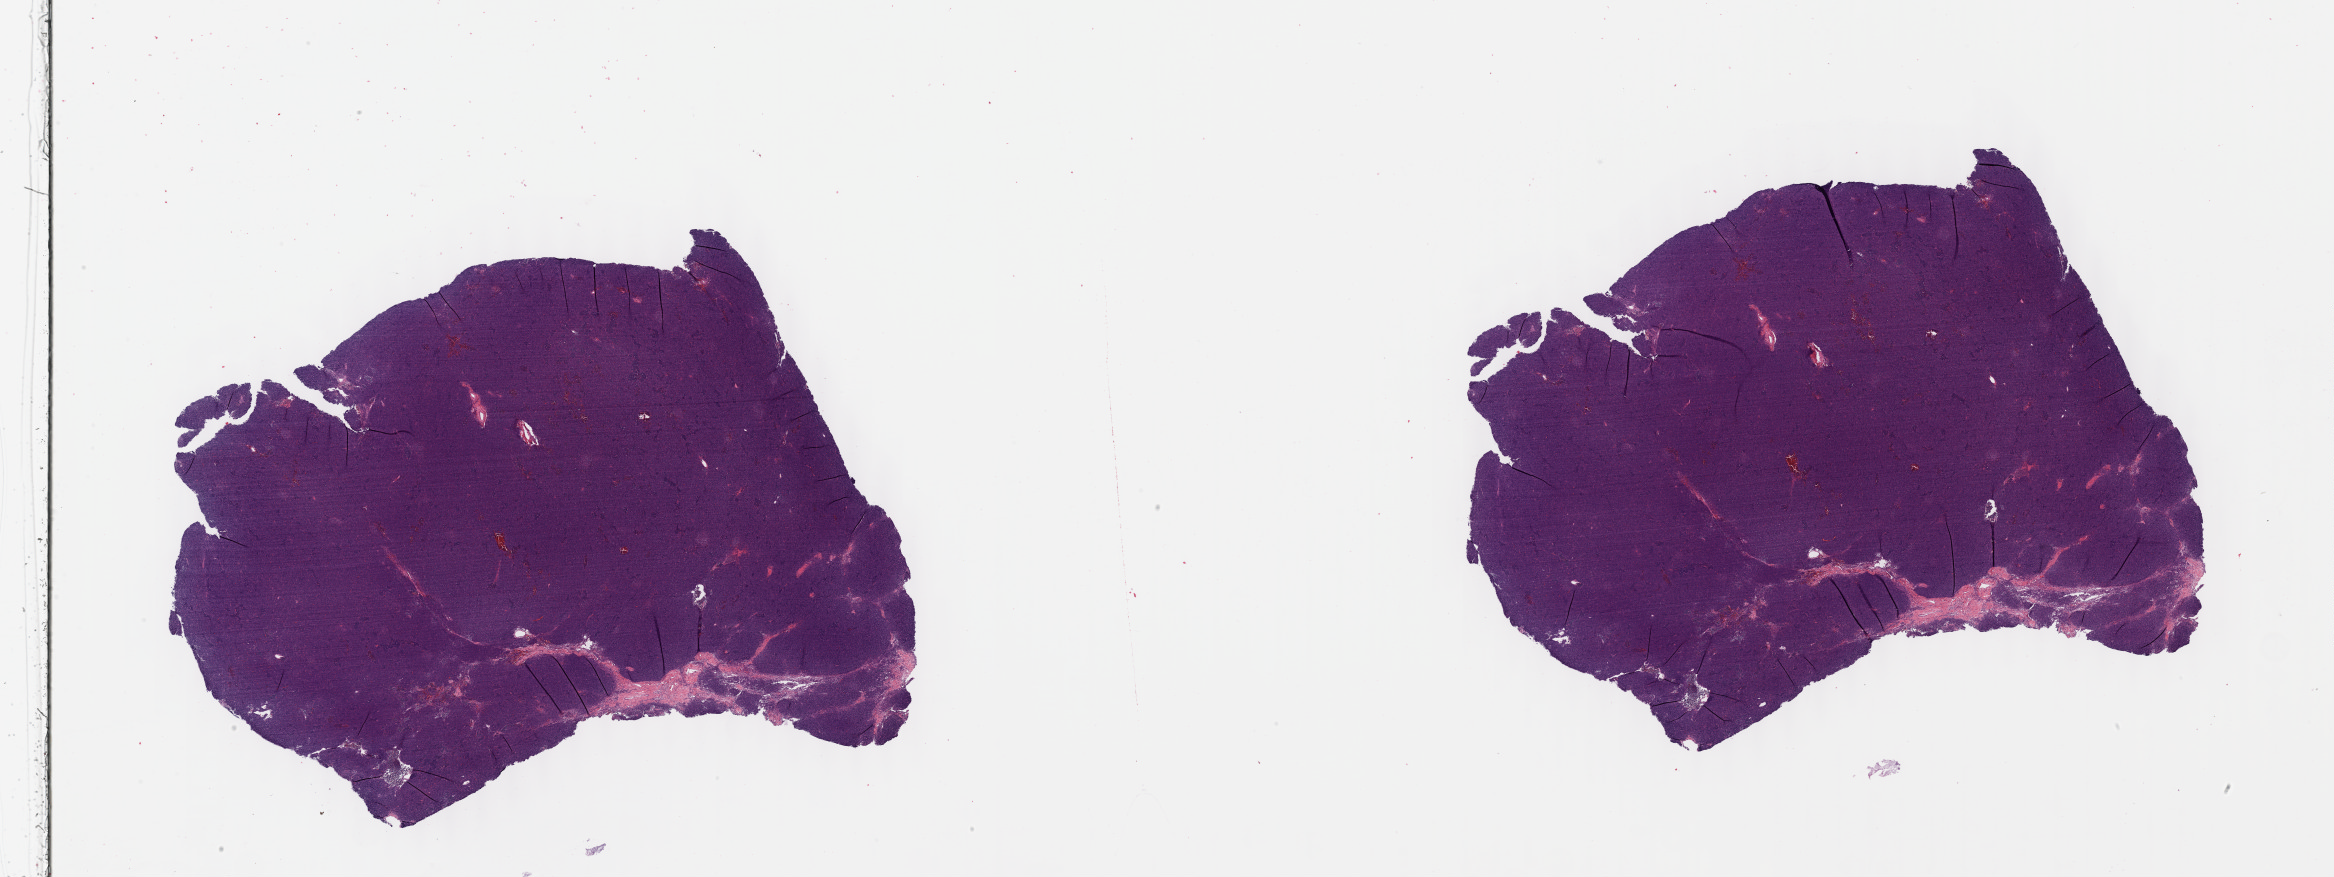
H&E whole-slide image, shown as a low-resolution overview of the whole scanned area (about 37.8 x 14.2 mm, acquisition: 40x scan). Formalin-fixed paraffin-embedded (FFPE) diagnostic section. Thymus, primary tumour sample. Female patient; age at initial diagnosis 54 years.
• histologic diagnosis: Thymoma, type B1, malignant